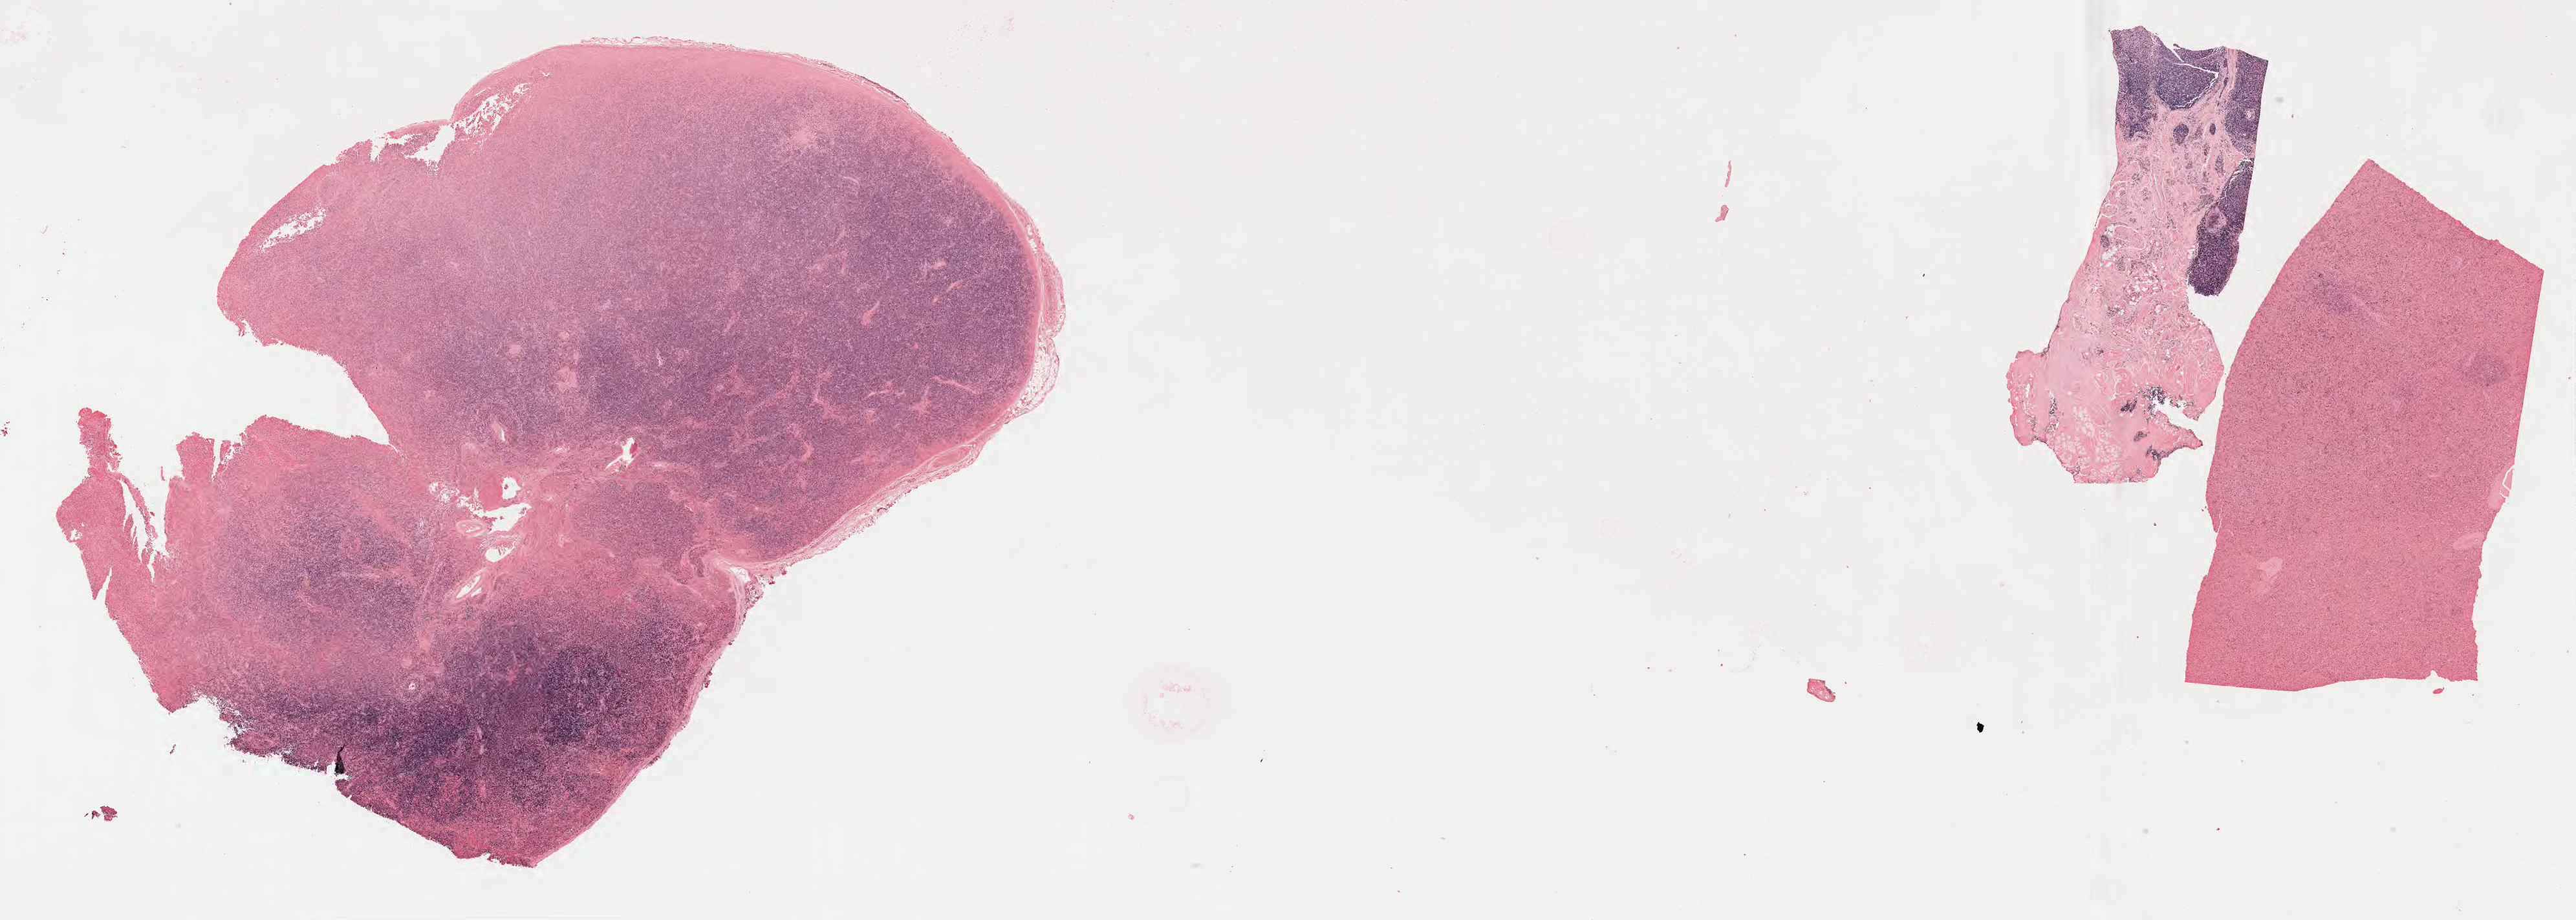
Whole-slide image; stain recorded as Iodonitrotetrazolium — whole scanned area (about 32.2 x 11.5 mm) shown as a low-resolution overview; tumor tissue; site: lymph node. Patient: male, 32 years old.
- histologic diagnosis: Diffuse large B-cell lymphoma, NOS